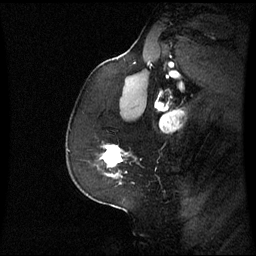
Breast MRI (dynamic contrast-enhanced), one sagittal slice; position 44 of 60 along the scan axis; dynamic contrast-enhanced series, image 2 of 3 at this slice position (ordered by acquisition); 1.5 T; TE 4.2 ms, TR 8.9 ms; 2.4 mm slice thickness; 256 × 256 image matrix. Patient: female, 59 years. From the clinical record (not read from this slice): setting: breast cancer imaged before/during neoadjuvant chemotherapy; receptor status: triple-negative.
Structures marked on this image (semi-automatically segmented with operator editing):
- analysis volume of interest (the breast-tissue region the enhancement analysis was run in; not a lesion): box from (x=98, y=145) to (x=134, y=183) px
- tumour enhancement mask (voxels above the 70 % enhancement threshold inside the analysis volume of interest): (x=102, y=145)–(x=122, y=177)